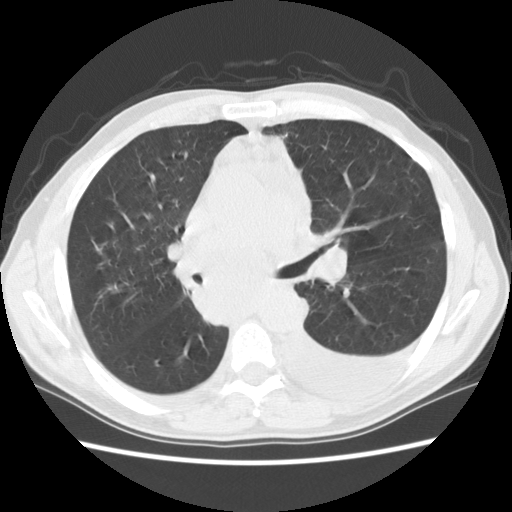
Low-dose screening chest CT, axial slice; baseline annual screen; lung window (W 1500 / L -600 HU); standard (soft-tissue) reconstruction kernel (STANDARD); 140 kVp; slice 50 of 135 in the series; 512 × 512 image matrix, field of view 346 × 346 mm. Male, age 60 years at enrolment. Current smoker at enrolment.
Expert reader's lesion annotation, bounding box [x1, y1, x2, y2] px = [176, 238, 297, 329]. No non-calcified nodule or mass ≥4 mm was recorded by the screening reader at this exam. Lung cancer was diagnosed 12 days after this screen: squamous cell carcinoma, NOS, carina, poorly differentiated (G3), stage IV (AJCC 6th edition).